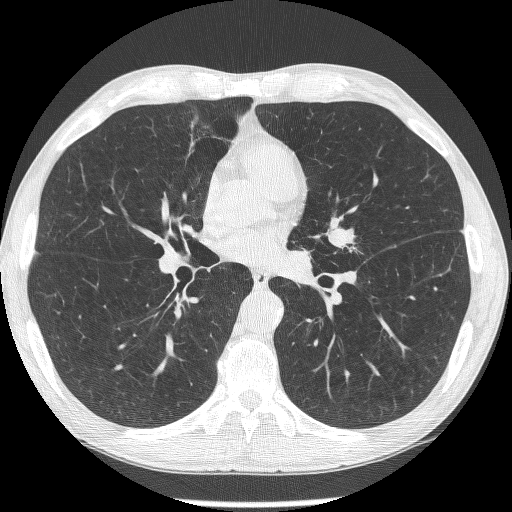
Low-dose screening chest CT, axial slice, second screening round (one year after baseline), lung window (W 1500 / L -600 HU), lung (sharp) reconstruction kernel (BONE), slice 138 of 293 in the series. Male, age 62 years at enrolment. Former smoker at enrolment.
Expert-annotated lung lesion, bounding box (x1, y1, x2, y2) in pixels: (319, 217, 368, 265). The screening reader recorded 2 non-calcified nodules or masses ≥4 mm on this exam (lingula, lingula); which of them this box marks is not recorded. Official screen result: positive, other. Later outcome: lung cancer diagnosed 95 days after this screen — small cell carcinoma, NOS, left upper lobe, stage IIIA (AJCC 6th edition).